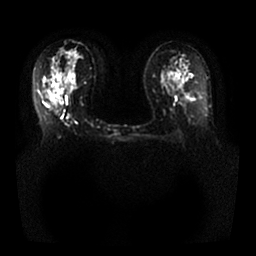
Breast MRI, one axial slice. Position 14 of 25 along the scan axis. Diffusion-weighted series; image 2 of 4 stored at this slice position (different b-values; order by instance number). 1.5 T. 4 mm slice thickness. 256 × 256 image matrix, field of view 350 × 350 mm. Female patient.
Structures marked on this image (outlined manually by an expert reader):
- tumour on diffusion-weighted imaging: box from (x=53, y=105) to (x=63, y=112) px